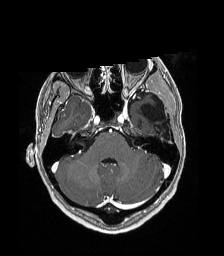
Brain MRI from a brain-tumour surgery series, one axial slice. Slice 131 of 192 in the series (ordered by position). T1-weighted post-contrast. 1 mm slice thickness. 224 × 256 image matrix, field of view 224 × 256 mm. From the clinical record (not read from this slice): histopathology: Low grade glioma; IDH mutation: no.
Outlined on this slice (outlined manually by an expert reader):
- previous resection cavity: bounding box [x1, y1, x2, y2] px = [142, 98, 169, 138]